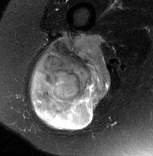
MRI of an extremity soft-tissue mass, one axial slice; position 42 of 77 along the scan axis; T2-weighted fat-saturated; MR volume resampled by the dataset authors to the PET/CT grid (not the native acquisition matrix); 153 × 156 image matrix, field of view 149 × 152 mm. Female patient. From the clinical record (not read from this slice): histological type: synovial sarcoma; grade: intermediate; site of the primary tumour: right buttock.
Structures marked on this image (expert contour drawn on MRI and transferred to this co-registered scan by the dataset authors):
- gross tumour volume including surrounding oedema: box from (x=30, y=33) to (x=111, y=130) px
- gross tumour volume (mass): (x=30, y=34)–(x=111, y=130)